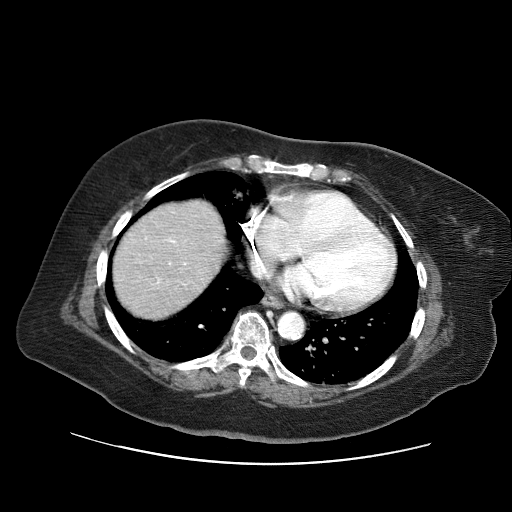
Contrast-enhanced abdominal CT (liver protocol), one axial slice; position 61 of 71 along the scan axis; 120 kVp; soft-tissue window (W 400 / L 40 HU); 2.5 mm slice thickness; 512 × 512 image matrix, field of view 400 × 400 mm. From the clinical record (not read from this slice): diagnosis: hepatocellular carcinoma (patient treated with transarterial chemoembolisation; whether this scan precedes or follows treatment is not stated here); TNM stage (as recorded): Stage-II; Child-Pugh class: A; tumour differentiation: poorly differentiated.
Outlined on this slice (semi-automatic segmentation, software-assisted and operator-edited):
- abdominal aorta: bounding box (x1, y1, x2, y2) in pixels: (278, 312, 303, 338)
- liver parenchyma outside the tumour (the mass and vessels are separate outlines, so this box may not span the whole liver): (112, 200, 224, 318)
- liver vessels: (157, 238, 185, 283)